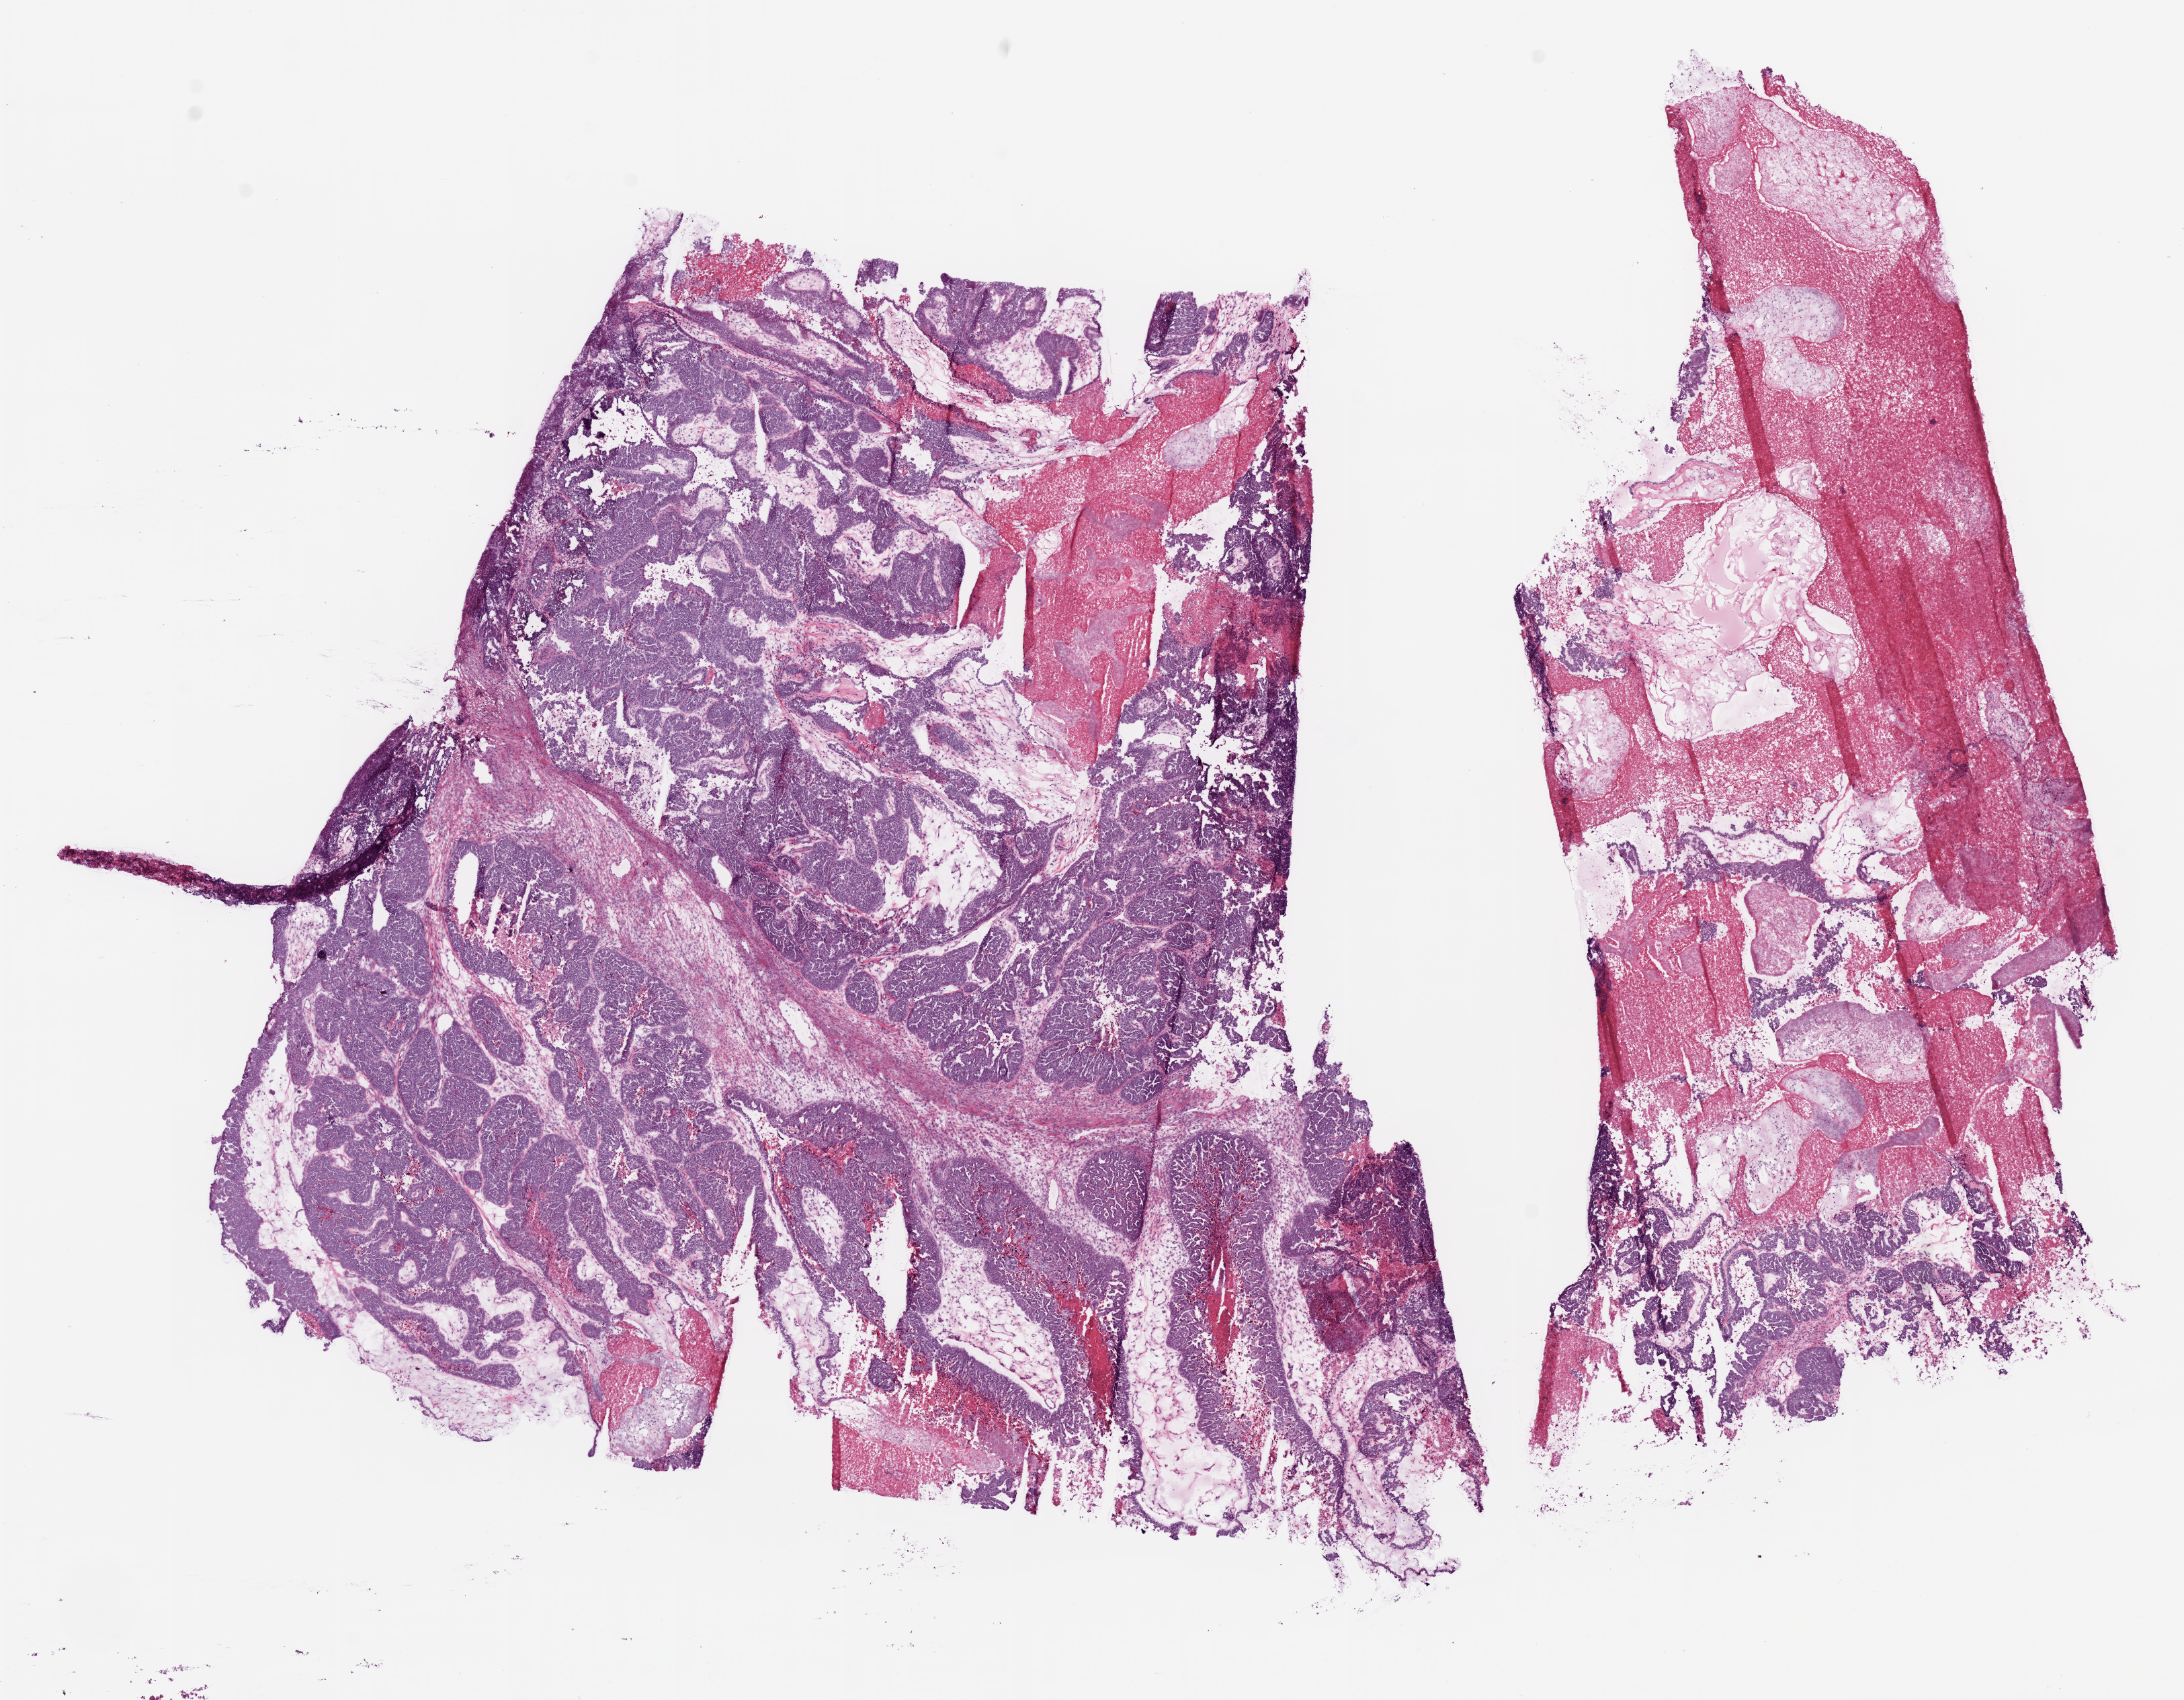
Digitized H&E tissue section (whole slide), a low-resolution overview of the entire scanned area, about 13.0 x 10.2 mm (from a 20x scan). Frozen section from the bottom of the tissue portion. Ovary, primary tumour sample. Female, age 51 years at initial diagnosis. Histologic grade: GX (grade cannot be assessed). Slide review estimates, as recorded: tumour cells 70%, tumour nuclei 90%, normal cells 0%, stromal cells 15%, necrosis 15%.
• pathologic diagnosis: Serous cystadenocarcinoma, NOS
• FIGO stage: IIIC